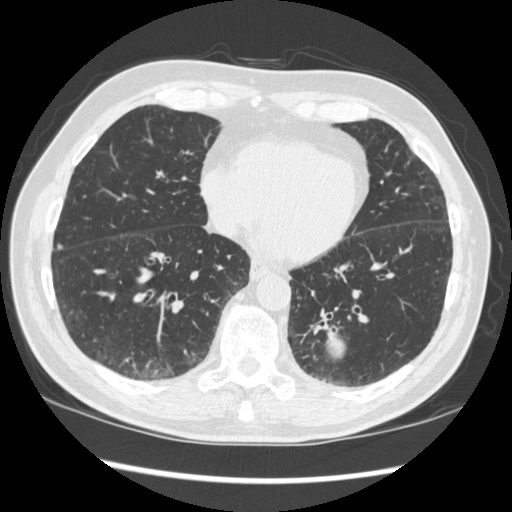
Chest CT (low-dose screening protocol), one axial image, first (baseline) screen, lung window (W 1500 / L -600 HU), 1.25 mm slice thickness, 512 × 512 image matrix. Male participant, aged 72 years at enrolment. Current smoker at enrolment.
• Expert reader's lesion annotation, bounding box [x1, y1, x2, y2] px = [274, 295, 378, 383].
• The screening reader recorded 2 non-calcified nodules or masses ≥4 mm on this exam (left lower lobe, right middle lobe); which of them this box marks is not recorded.
• Official screen result: positive, change unspecified: nodule(s) >= 4 mm or enlarging nodule(s), mass(es), or other non-specific abnormalities suspicious for lung cancer.